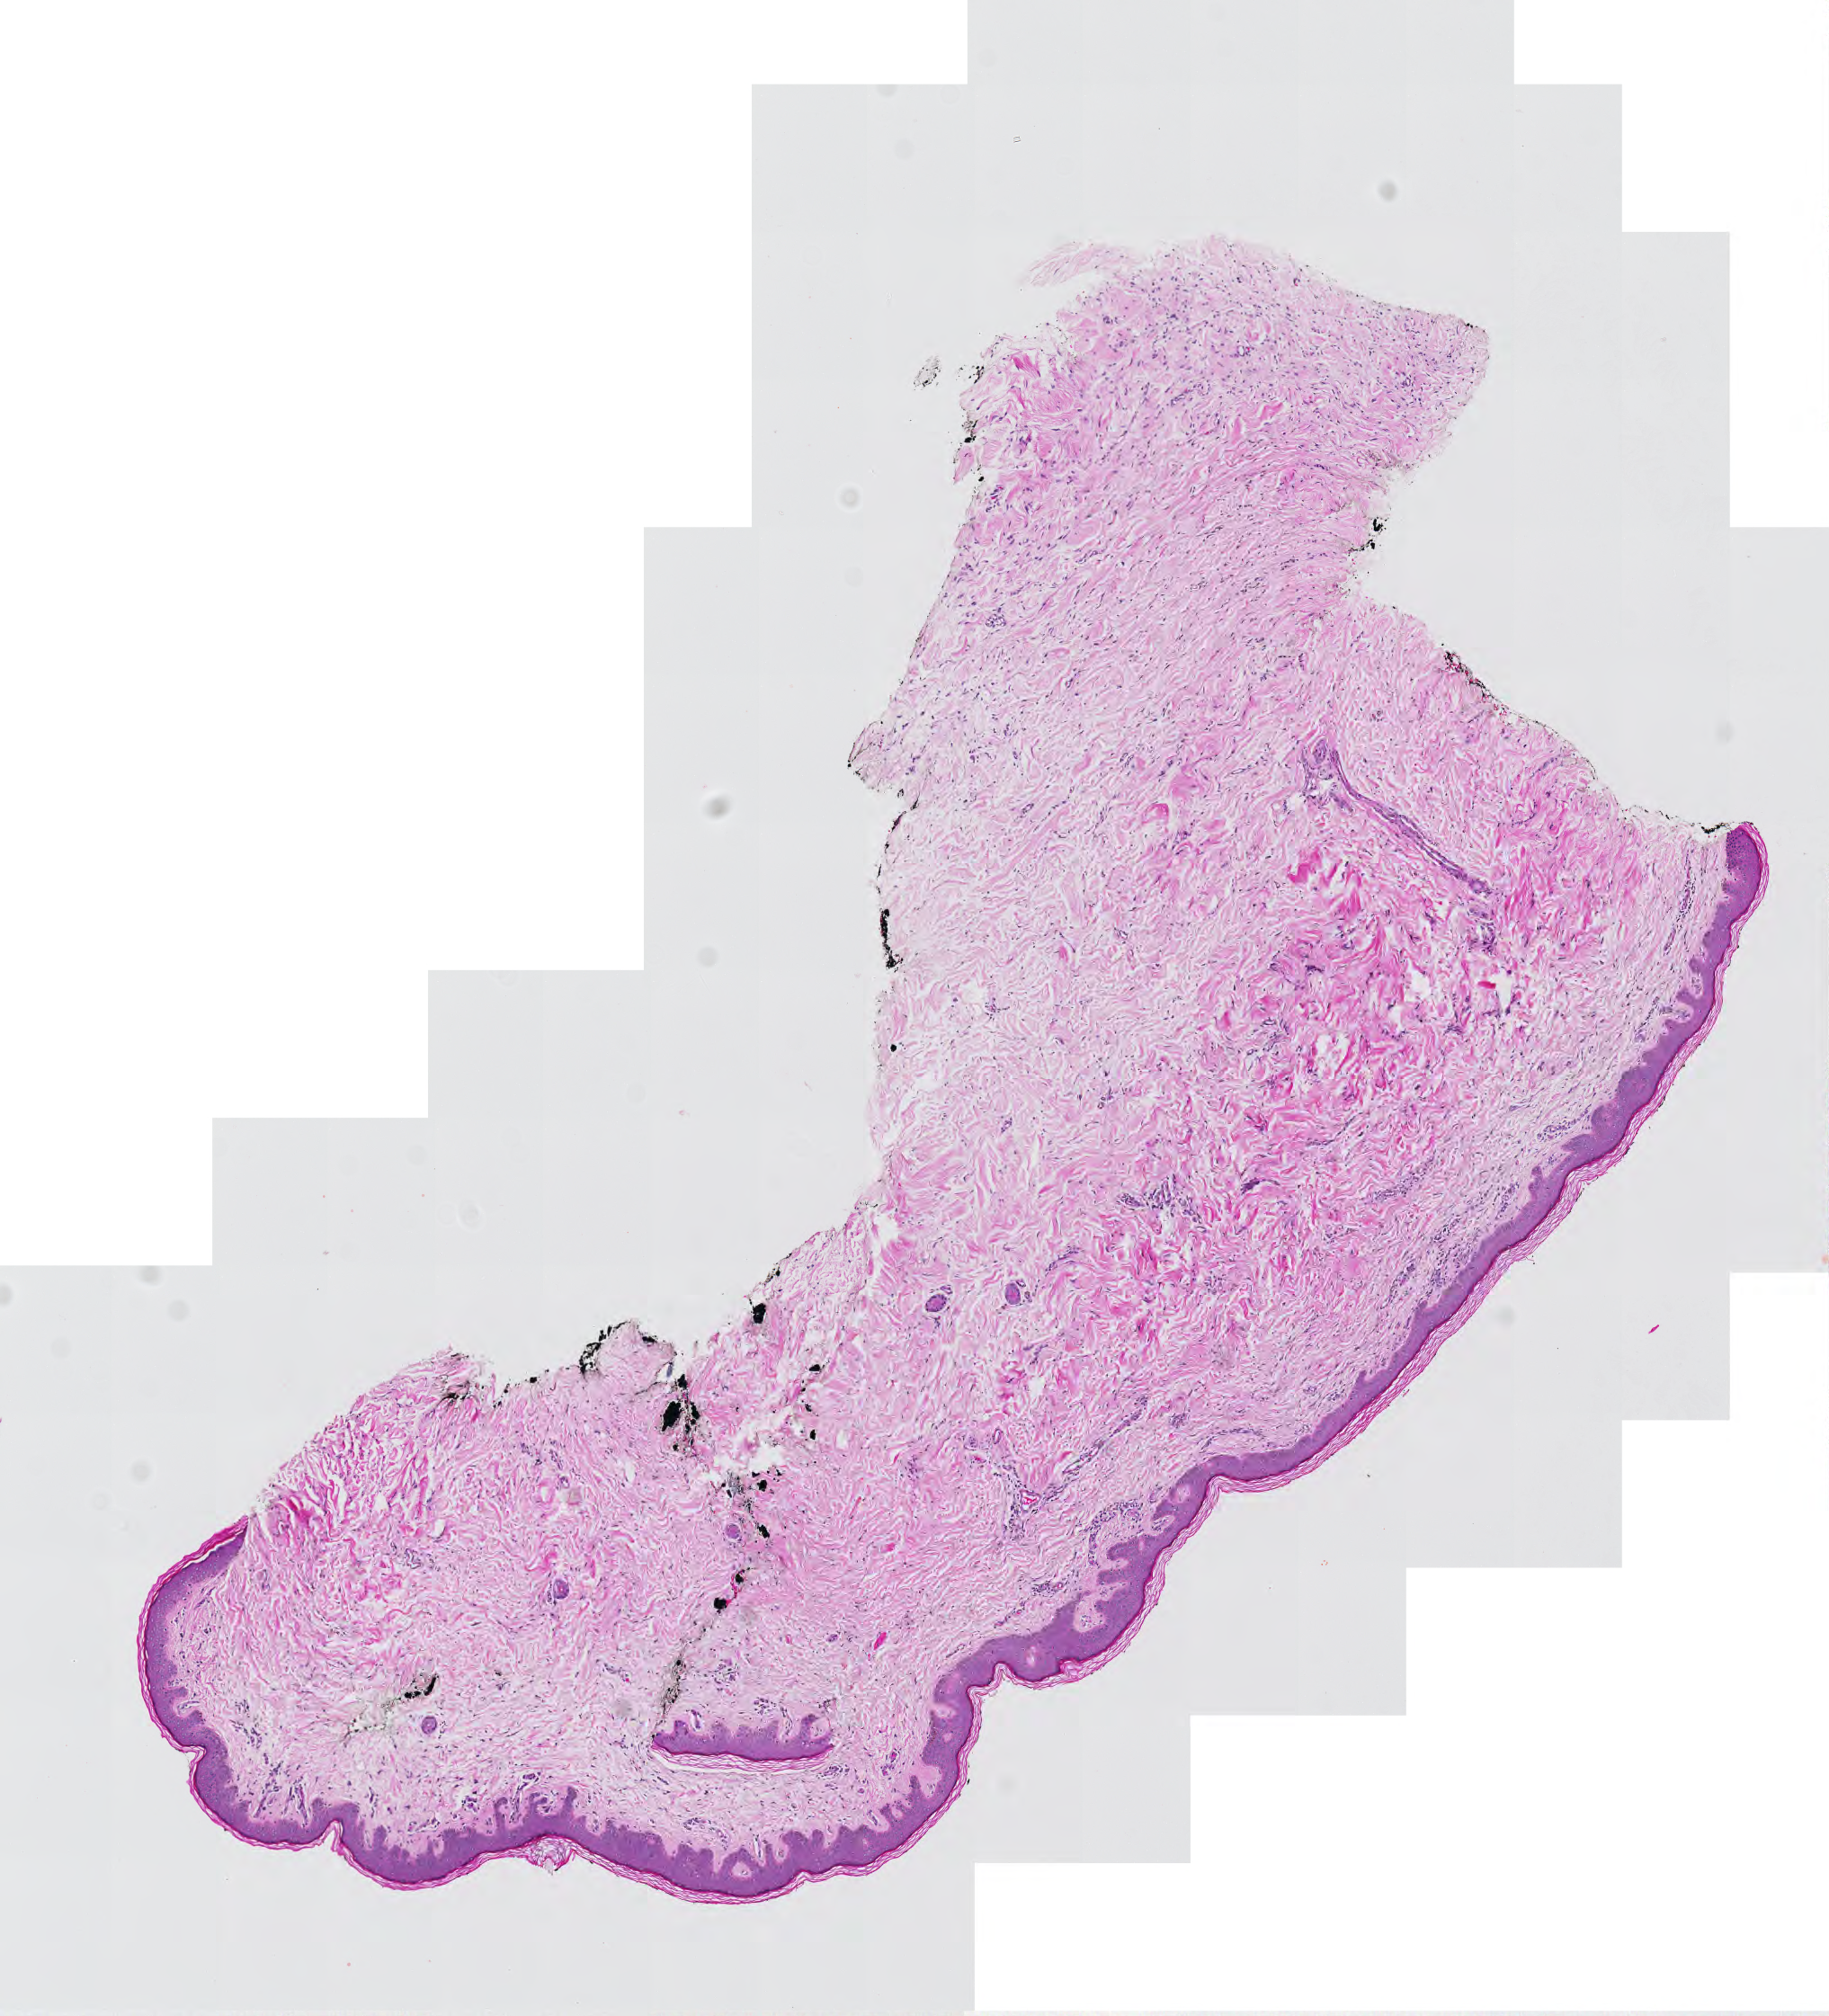
Whole-slide histology image, H&E-stained, a low-resolution overview of the entire scanned area, about 5.2 x 5.8 mm (acquisition: 20x scan), tumour tissue sample. Female, 72 y/o.
Patient diagnosis (cohort enrolment): sarcoma (site not recorded at cohort level).